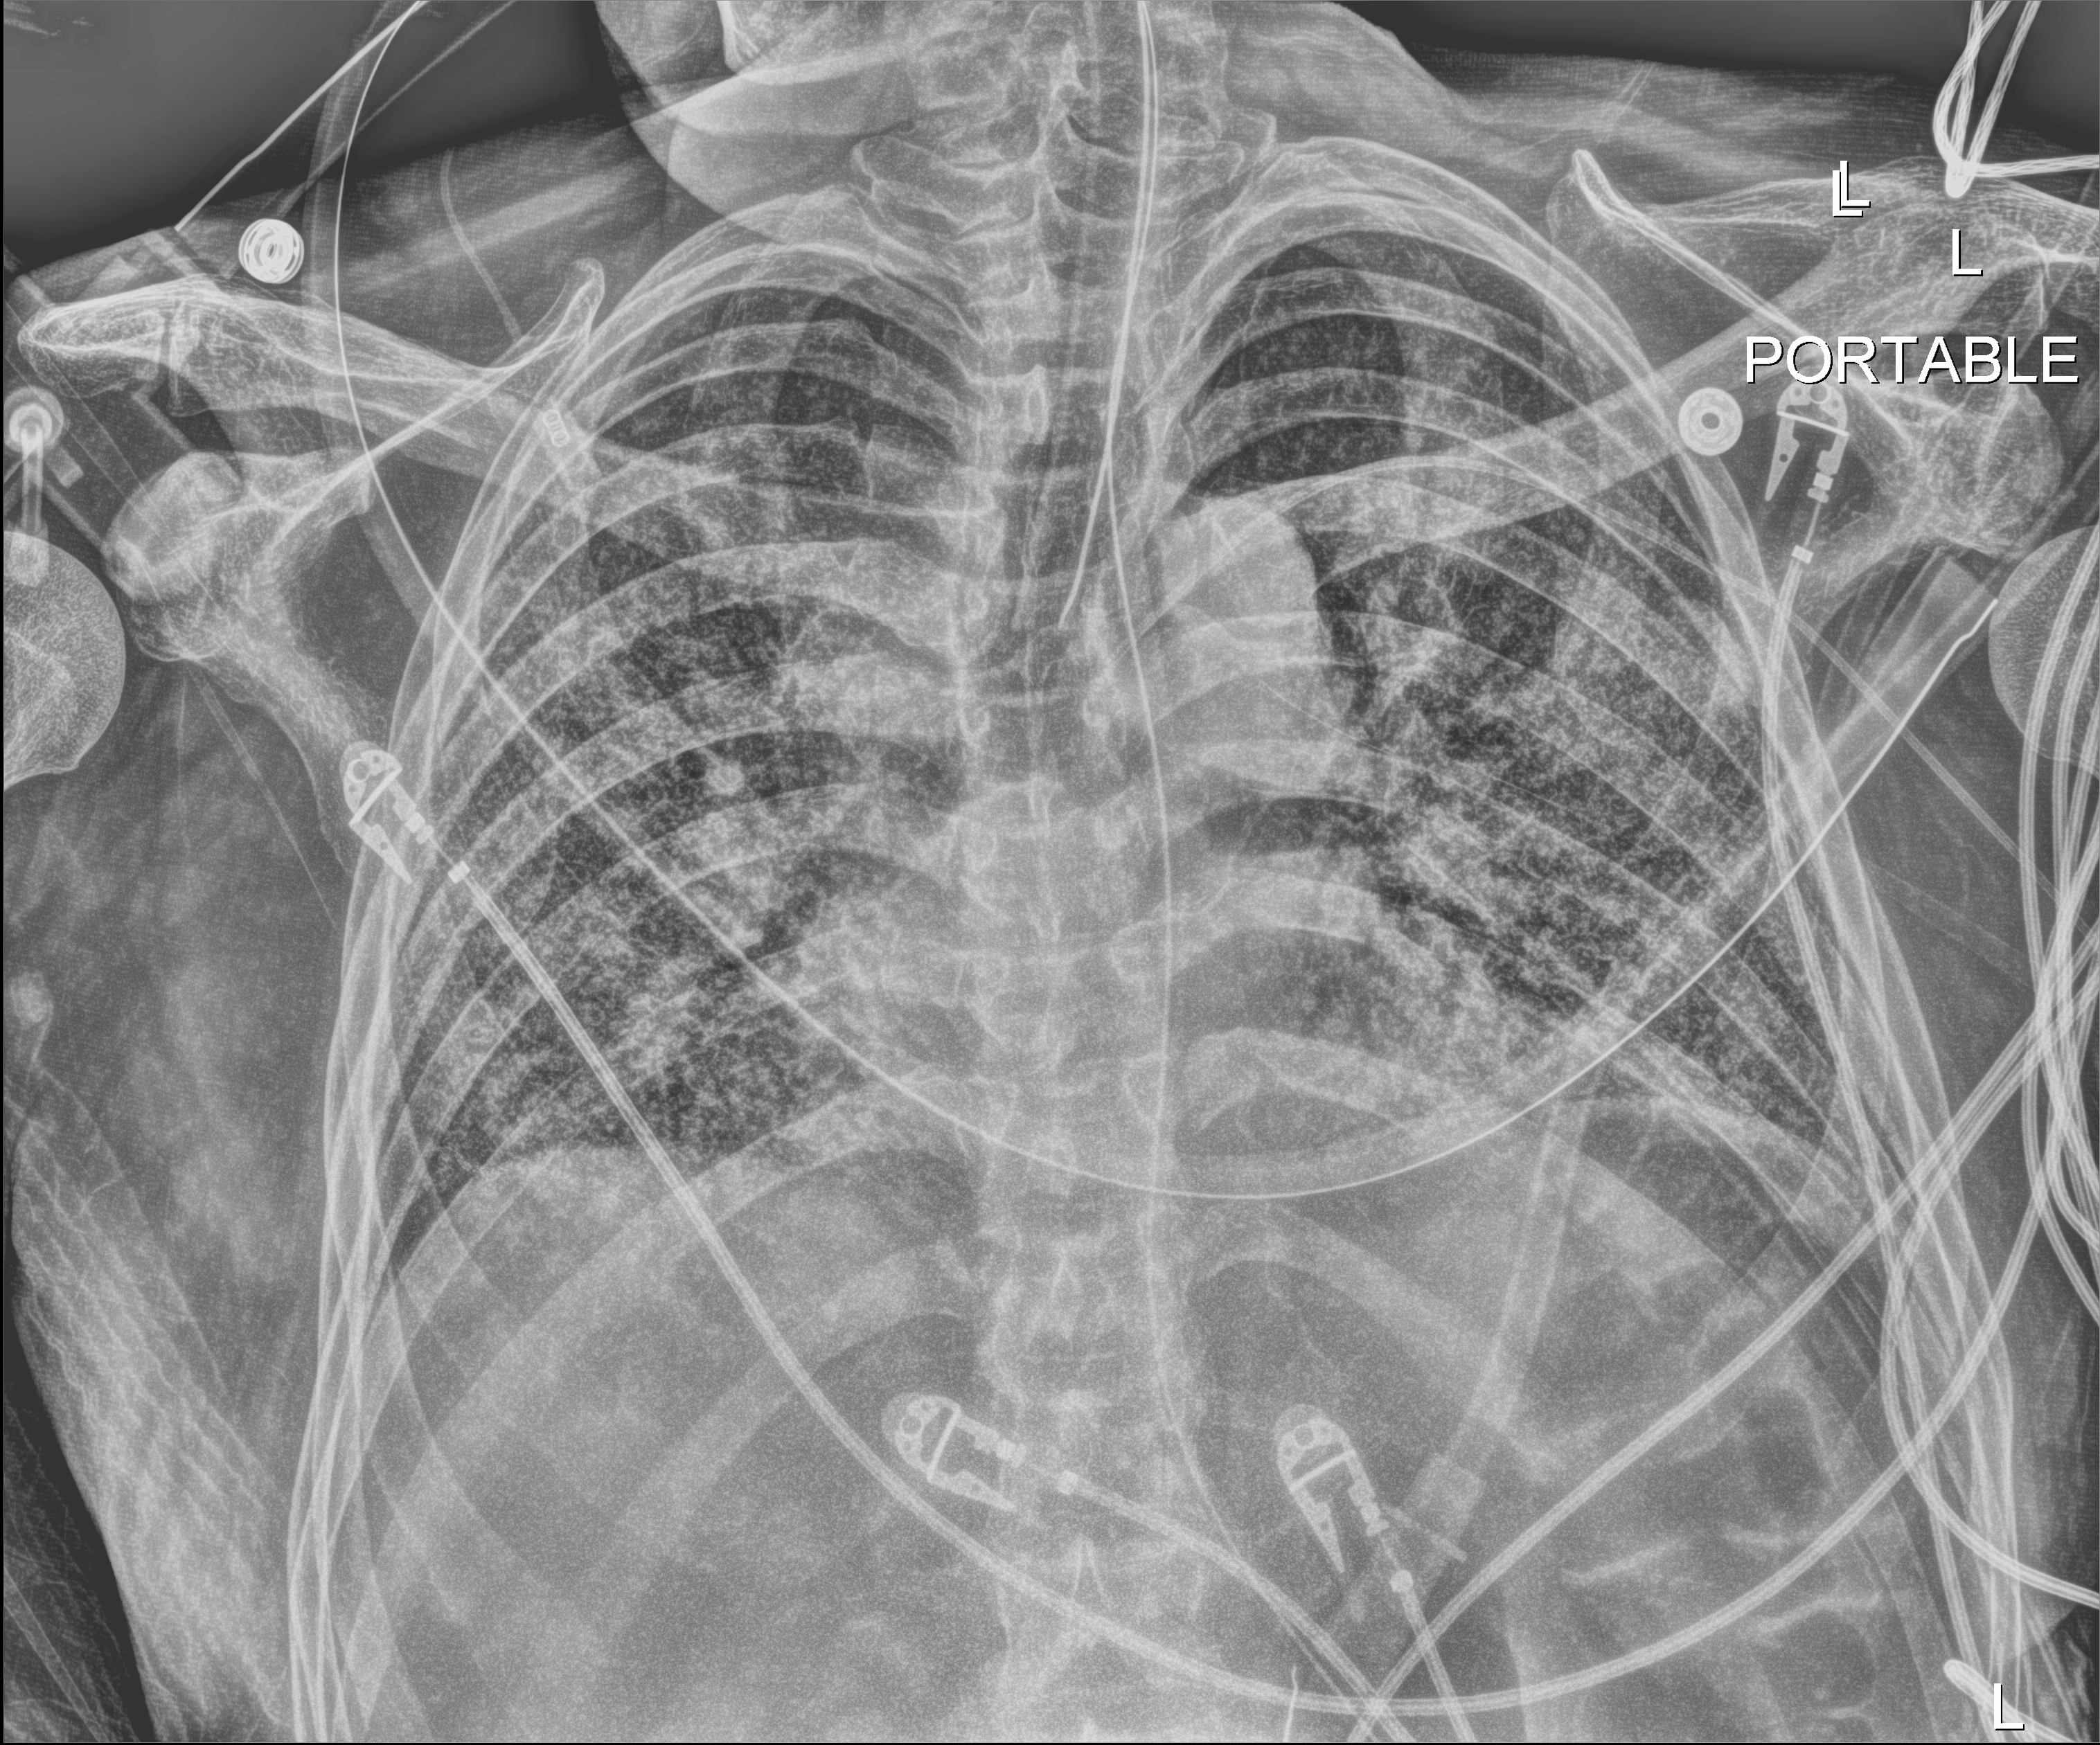
Chest radiograph, anteroposterior (AP) projection. Male patient hospitalised with COVID-19, age 60–74 years.
Admission-level facts for this patient (not findings on this image; timing relative to this image not recorded): admitted to intensive care during this hospital stay: yes; mechanically ventilated during this hospital stay: yes.